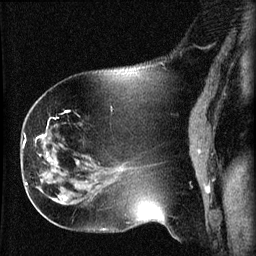
Breast MRI (dynamic contrast-enhanced), one sagittal slice; position 23 of 60 along the scan axis; dynamic contrast-enhanced series, image 2 of 3 at this slice position (ordered by acquisition); 1.5 T; TE 4.2 ms, TR 8.2 ms; 256 × 256 image matrix. Patient: female, 63 years.
Annotated regions visible in this slice (semi-automatic segmentation, software-assisted and operator-edited):
- analysis volume of interest (the breast-tissue region the enhancement analysis was run in; not a lesion): bounding box (x1, y1, x2, y2) in pixels: (22, 156, 64, 202)
- tumour enhancement mask (voxels above the 70 % enhancement threshold inside the analysis volume of interest): (59, 196, 61, 199)